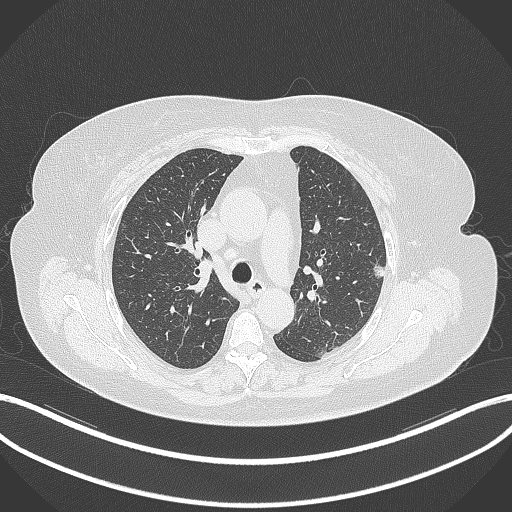
Chest CT, one axial slice; position 217 of 309 along the scan axis; reconstruction kernel B70f; 120 kVp; lung window (W 1500 / L -600 HU); 512 × 512 image matrix. Female patient, age 70 years. From the clinical record (not read from this slice): clinical TNM (as recorded): T1c N0 M0.
Structures marked on this image (bounding box drawn by a radiologist):
- lung tumour (recorded histology: adenocarcinoma): box from (x=369, y=258) to (x=390, y=283) px